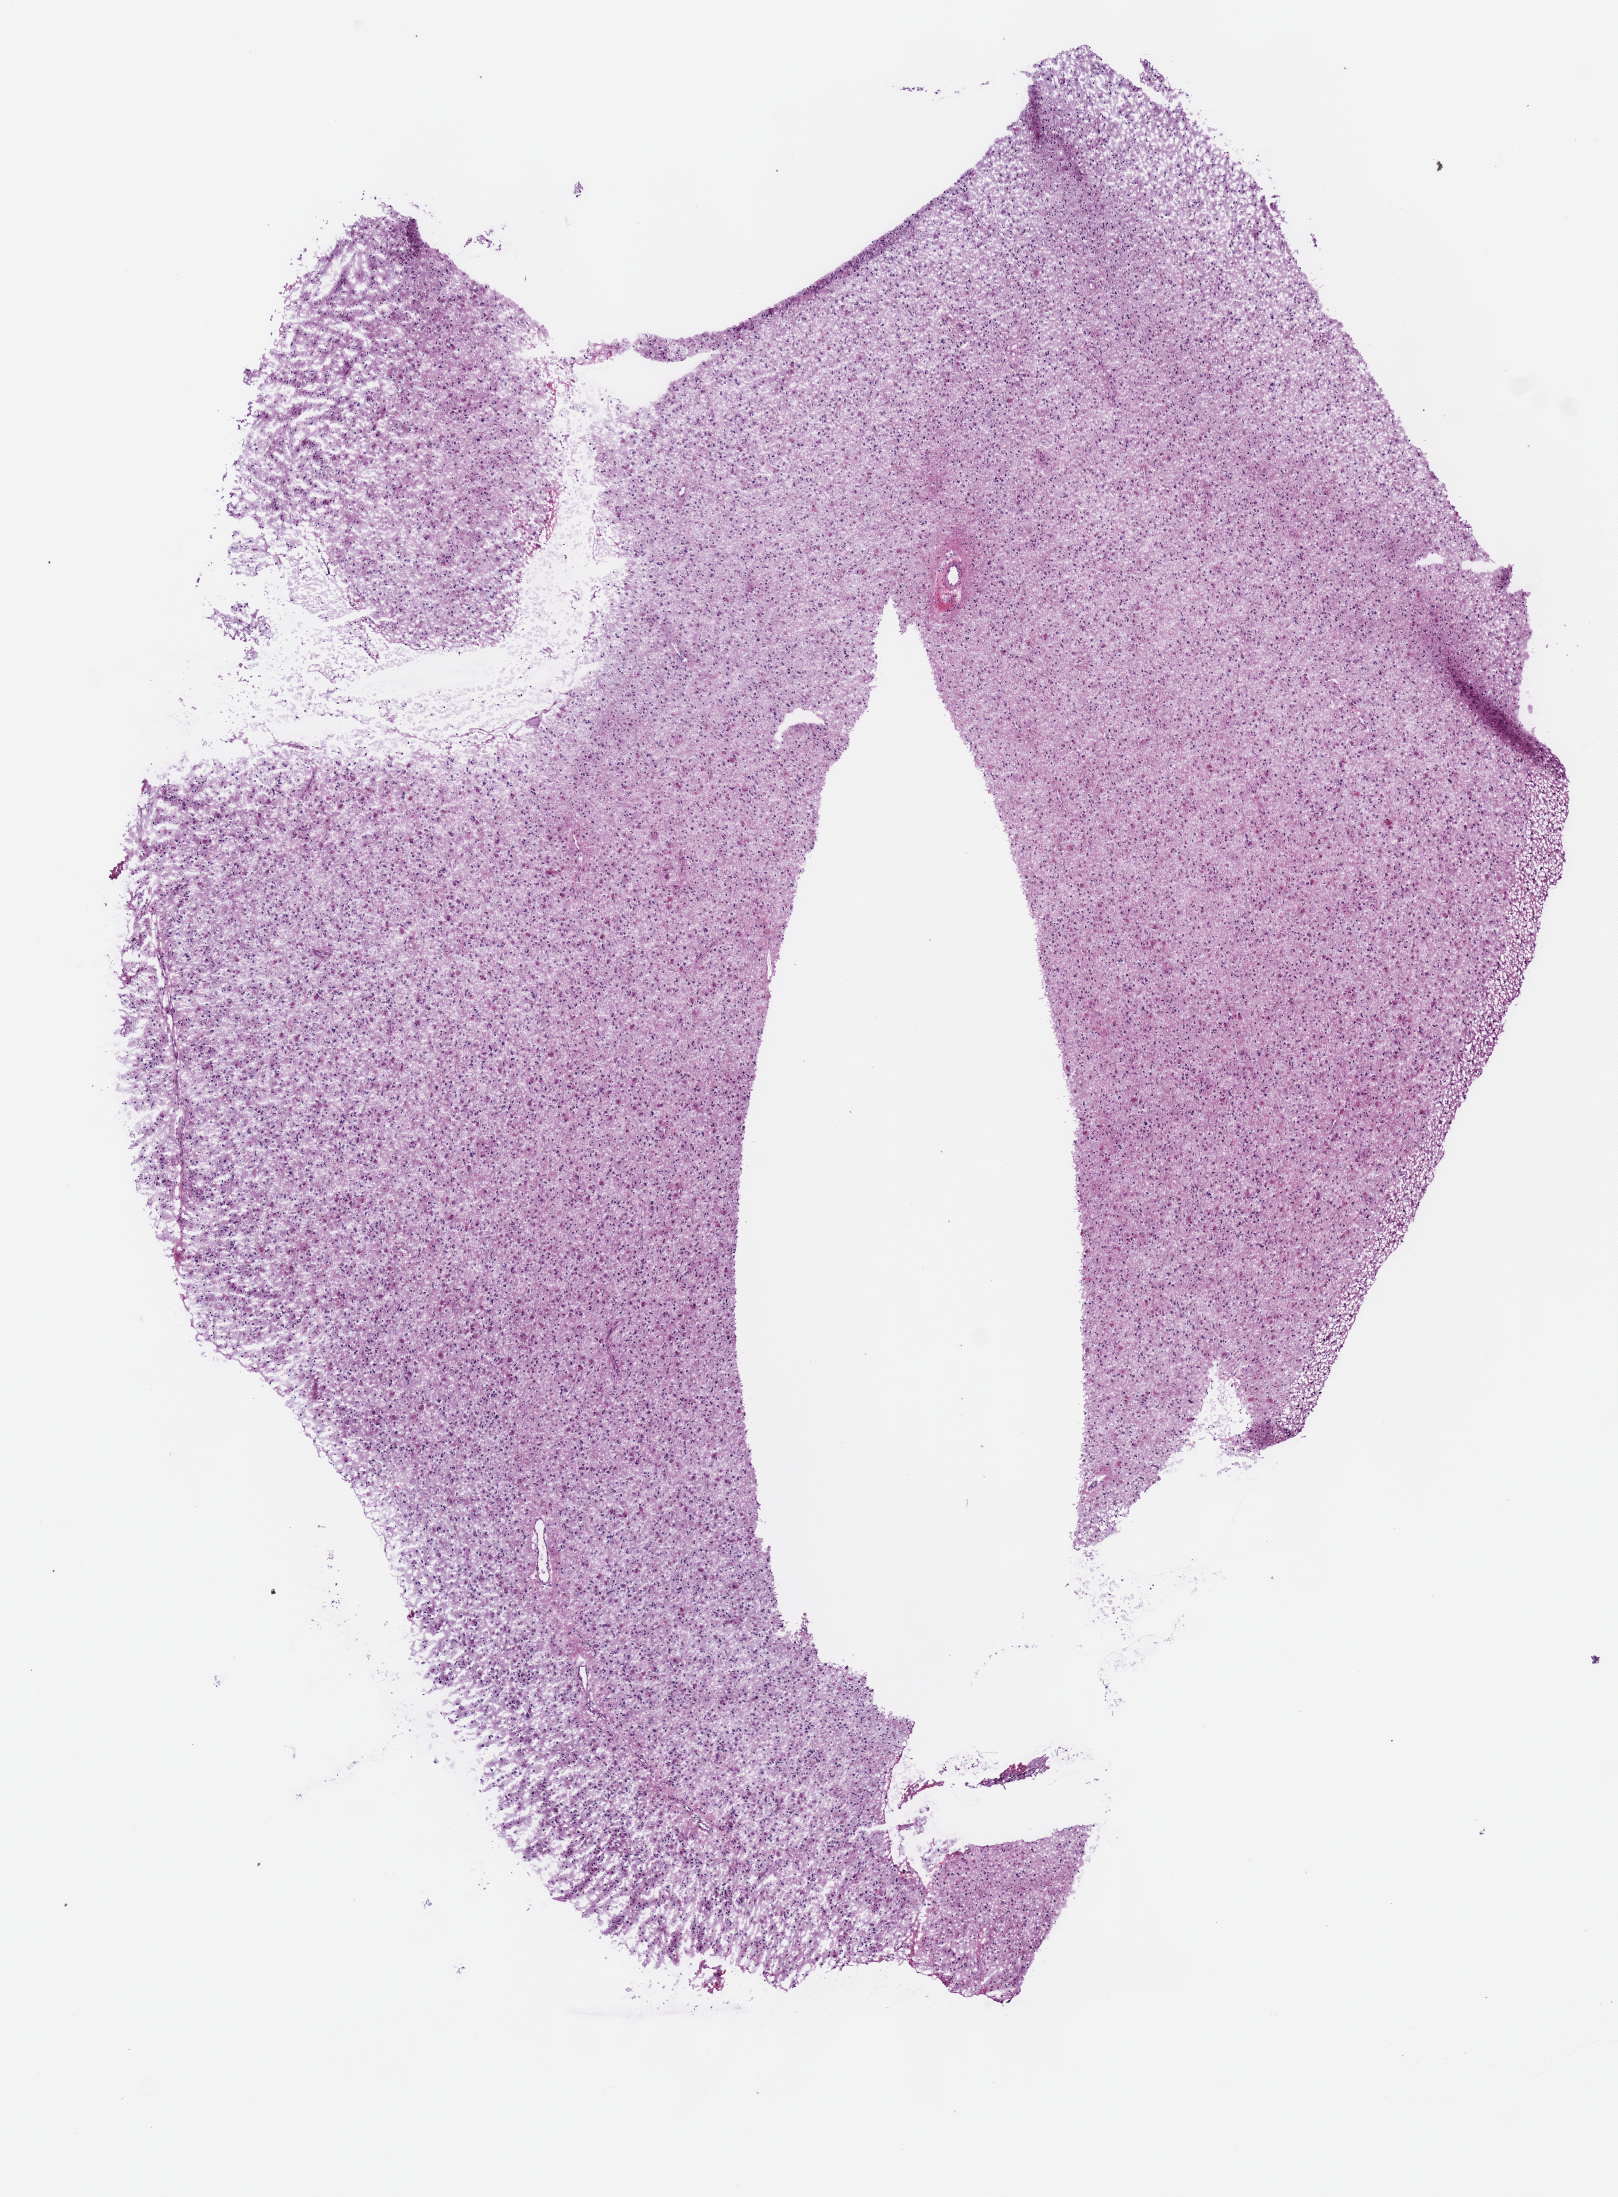
H&E-stained whole-slide image — whole scanned area (about 6.4 x 8.6 mm, acquisition: 40x scan) shown as a low-resolution overview. Frozen section from the bottom of the tissue portion. Brain, primary tumour sample. Female patient; age at initial diagnosis 29 years. Histologic grade: G3 (poorly differentiated). Pathologist review of this section (percent, as recorded): tumour cells 100%, tumour nuclei 70%, normal cells 0%, stromal cells 0%, necrosis 0%.
- diagnosis: Astrocytoma, anaplastic
- laterality: left